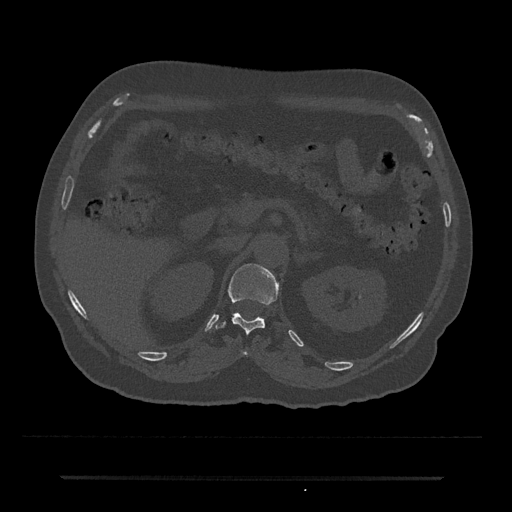
CT including the spine, one axial slice; position 124 of 797 along the scan axis; bone window (W 1800 / L 400 HU); 0.5 mm slice thickness; 512 × 512 image matrix, field of view 437 × 437 mm. Patient: male, 69 years. From the clinical record (not read from this slice): primary cancer: prostate.
Annotated regions visible in this slice (semi-automatic segmentation, software-assisted and operator-edited):
- T11 vertebra: bounding box (x1, y1, x2, y2) in pixels: (241, 351, 248, 357)
- T12 vertebra: (215, 264, 279, 334)